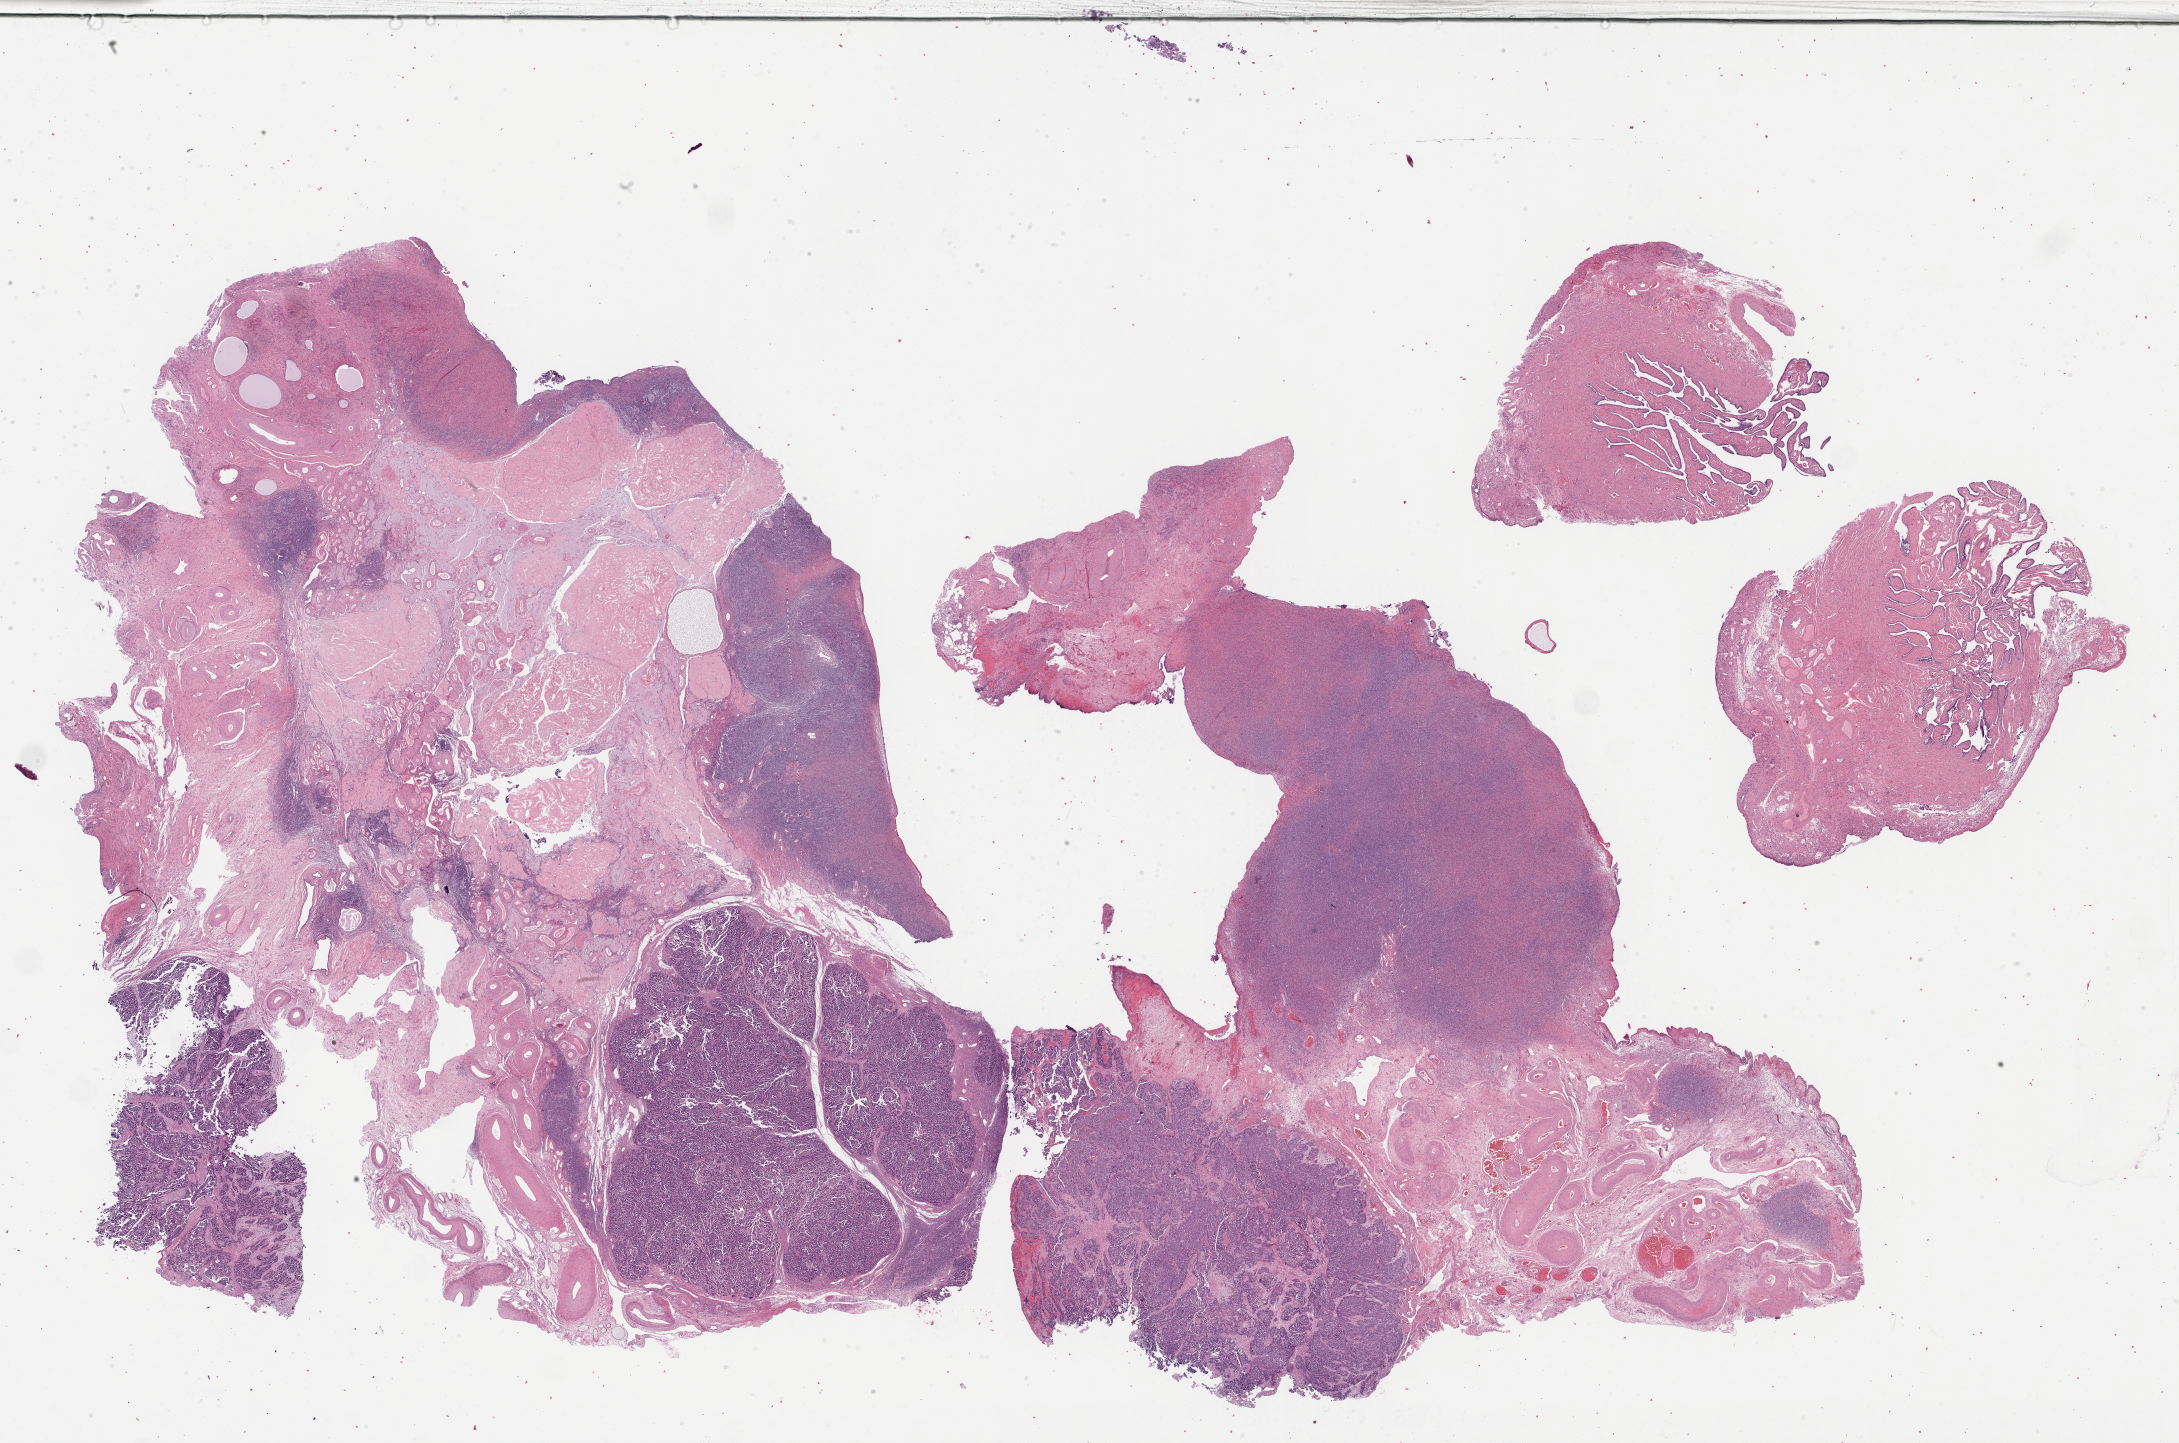
Whole-slide histology image, Hematoxylin and eosin (H&E) stained, whole scanned area (about 35.2 x 23.3 mm) shown as a low-resolution overview. Formalin-fixed paraffin-embedded (FFPE) diagnostic section. Sample: primary tumour, ovary. Female patient; age at initial diagnosis 76 years. Histologic grade: G3 (poorly differentiated).
FIGO stage: IIIC. Histologic diagnosis: Serous cystadenocarcinoma, NOS.